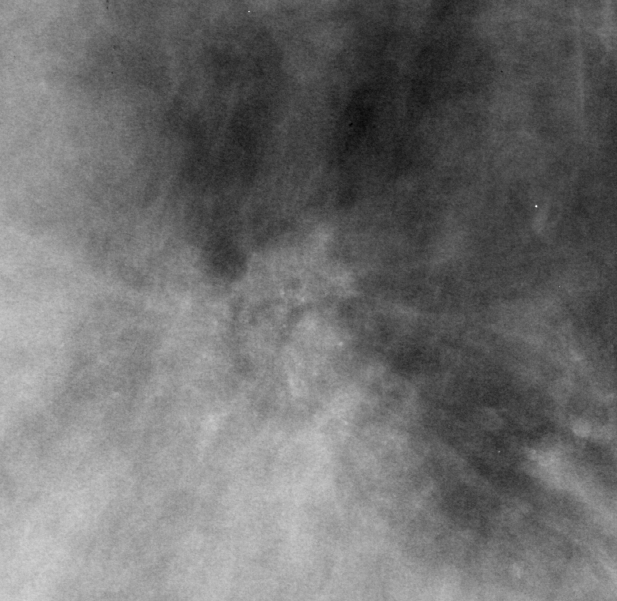
Crop from a digitized film mammogram around one marked abnormality; right breast; MLO view; BI-RADS breast density category 4 (scale 1–4).
Finding: calcifications, morphology punctate / pleomorphic, distribution clustered; BI-RADS assessment category 4; pathology (as recorded): malignant.